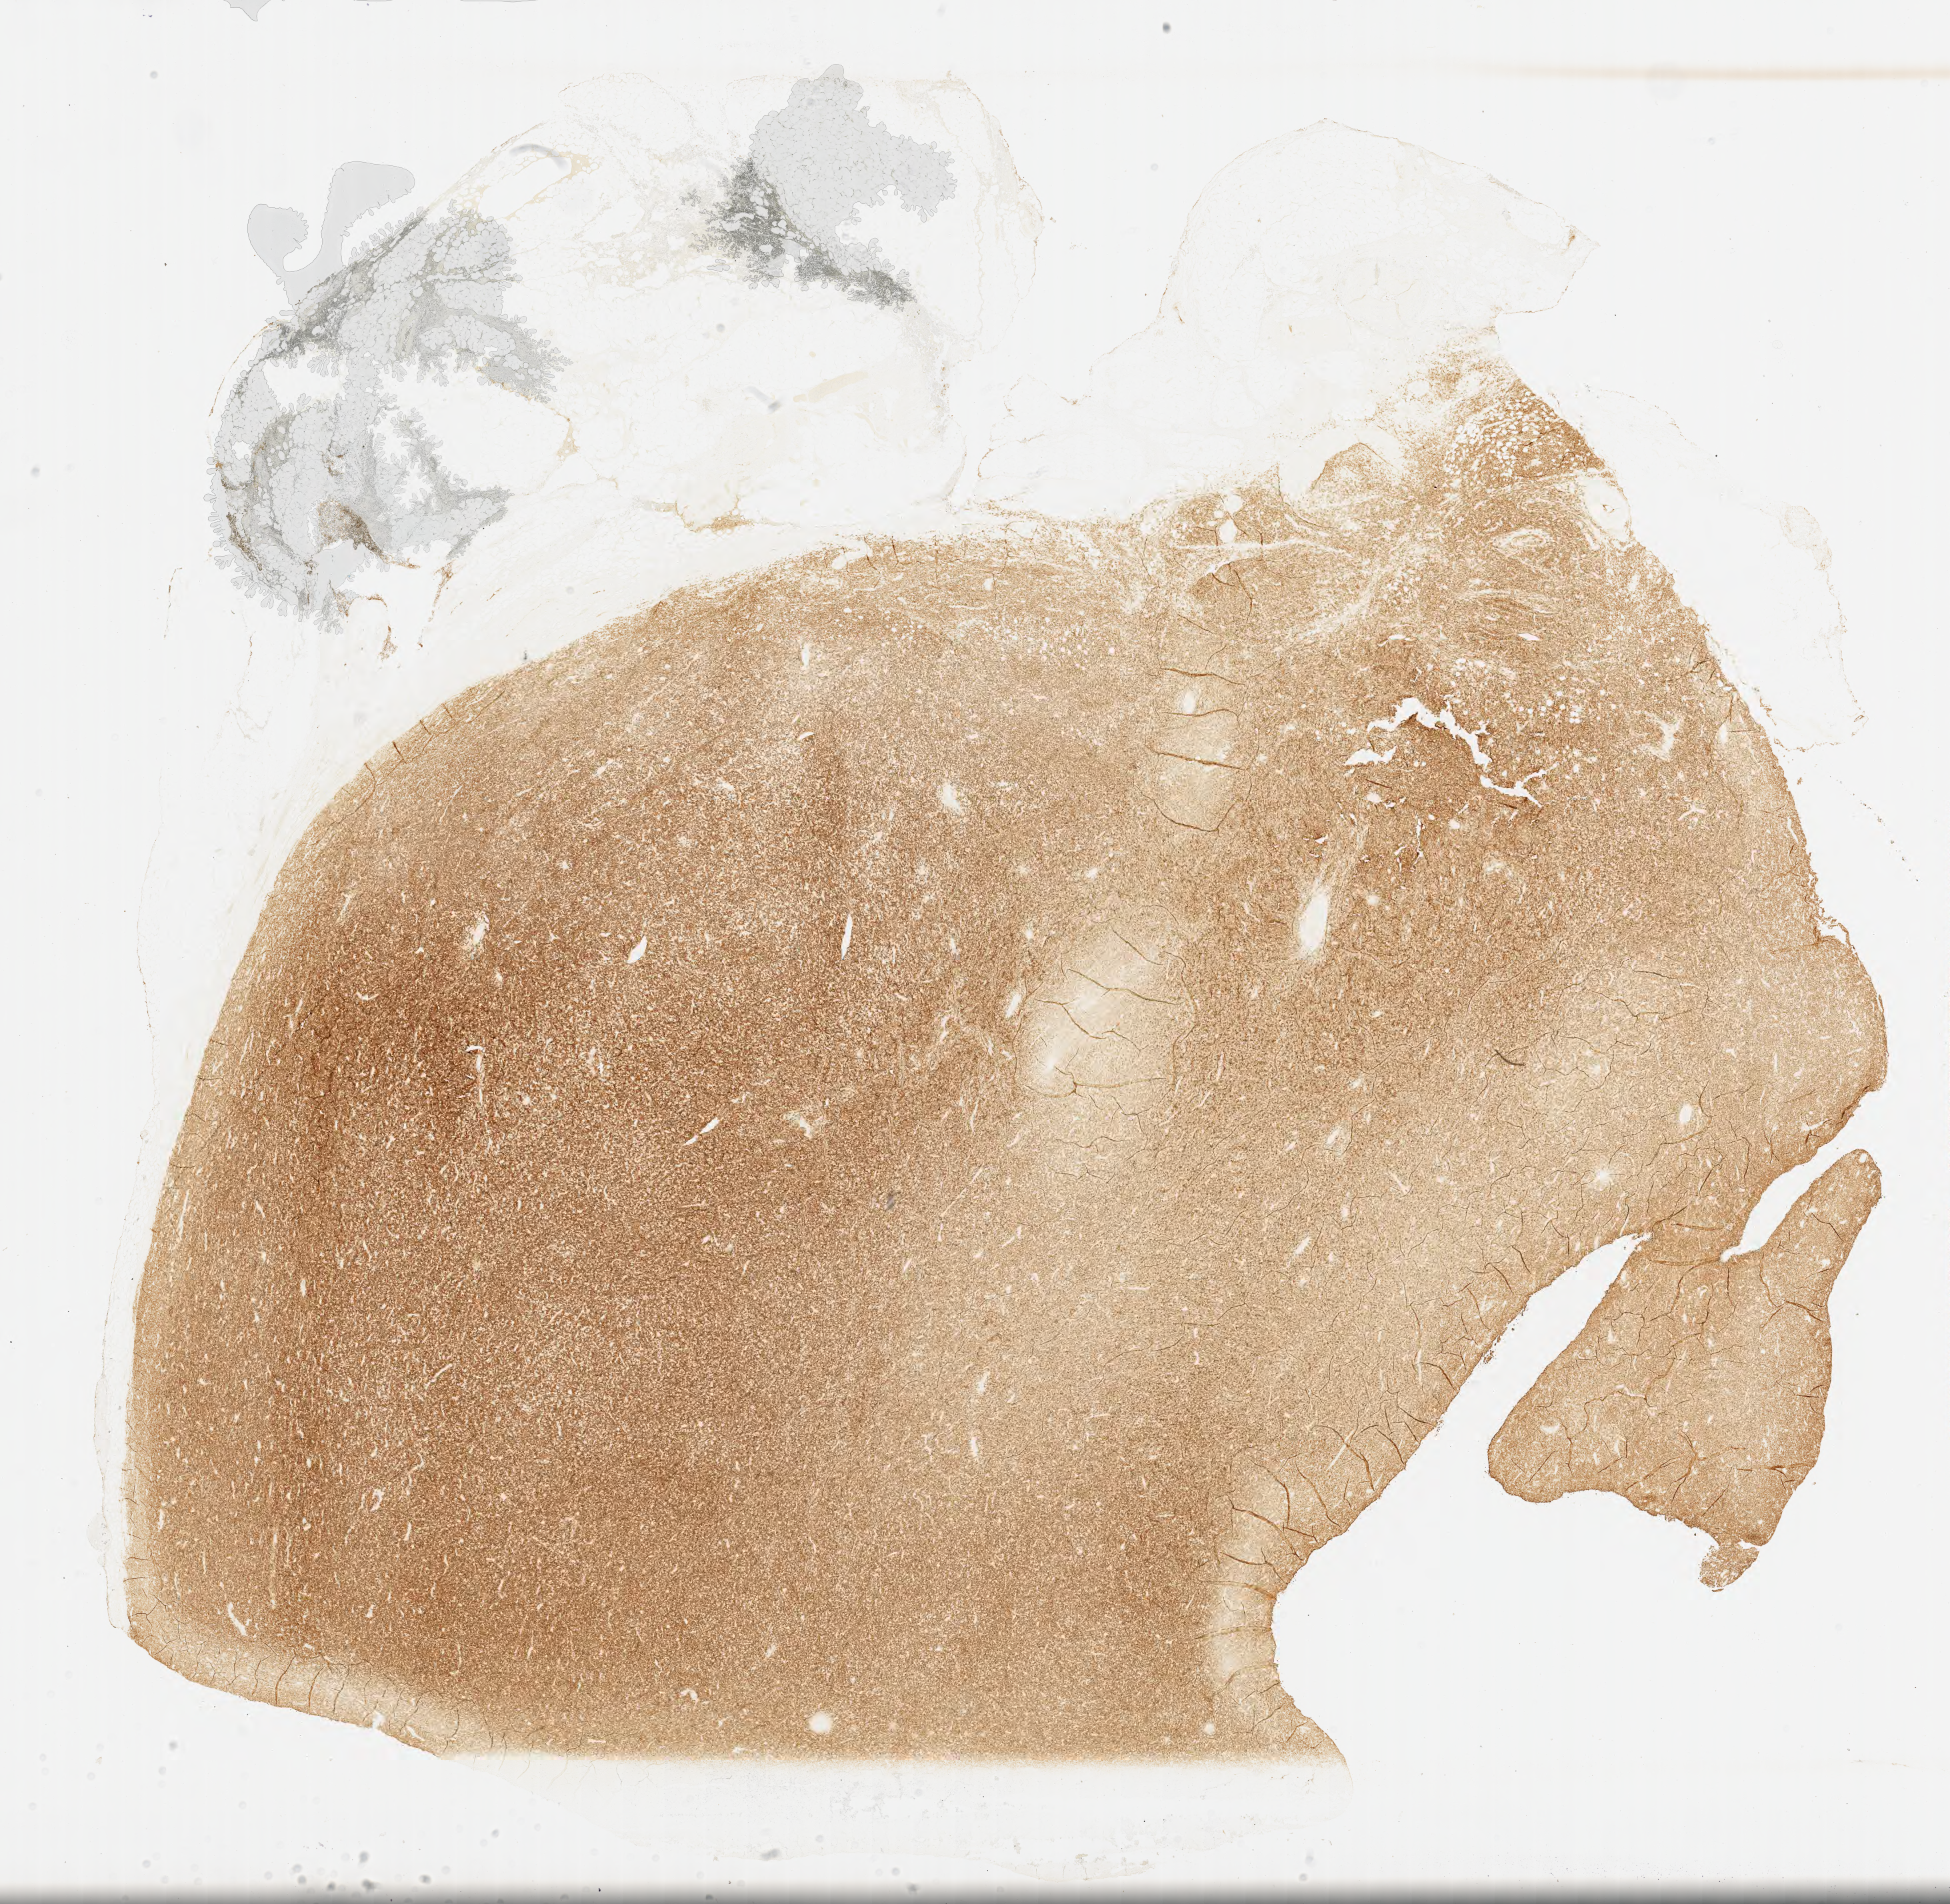
Whole-slide image, immunohistochemical stain for CD20, whole scanned area (about 23.6 x 23.1 mm) shown as a low-resolution overview, tumor tissue, site: lymph node. Patient: male, age 54 years.
Diagnosis: Diffuse large B-cell lymphoma, NOS.